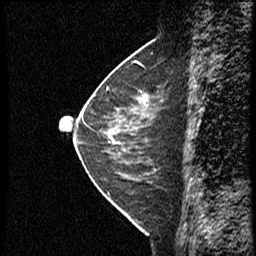
Breast MRI (dynamic contrast-enhanced), one sagittal slice; slice 15 of 40 in the series (ordered by position); dynamic contrast-enhanced study with each time point stored as its own series, time point 2 of 4 at this slice position (early post-contrast, ordered by acquisition time); 1.5 T; TE 4.2 ms, TR 18.8 ms; 3 mm slice thickness; 256 × 256 image matrix. Female patient. Case-level facts recorded for this patient, not image findings: setting: breast cancer imaged before/during neoadjuvant chemotherapy; receptor status: HER2-positive.
Annotated regions visible in this slice (semi-automatically segmented with operator editing):
- analysis volume of interest (the breast-tissue region the enhancement analysis was run in; not a lesion): box from (x=91, y=79) to (x=165, y=153) px
- tumour enhancement mask (voxels above the 100 % enhancement threshold inside the analysis volume of interest): (x=144, y=97)–(x=147, y=100)